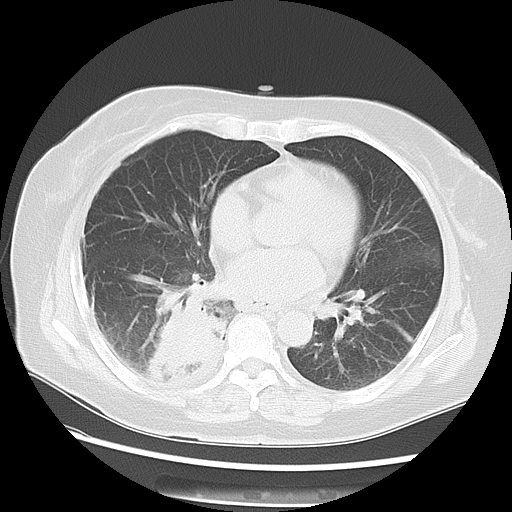
Chest CT, one axial slice; reconstruction kernel LUNG; lung window (W 1500 / L -600 HU); 5 mm slice thickness; 512 × 512 image matrix, field of view 350 × 350 mm. Female patient, age 69 years. From the clinical record (not read from this slice): clinical TNM (as recorded): T2 N1 M1a.
Annotated regions visible in this slice (rectangle marked by the reading radiologist):
- lung tumour (recorded histology: adenocarcinoma): bounding box (x1, y1, x2, y2) in pixels: (141, 298, 224, 398)